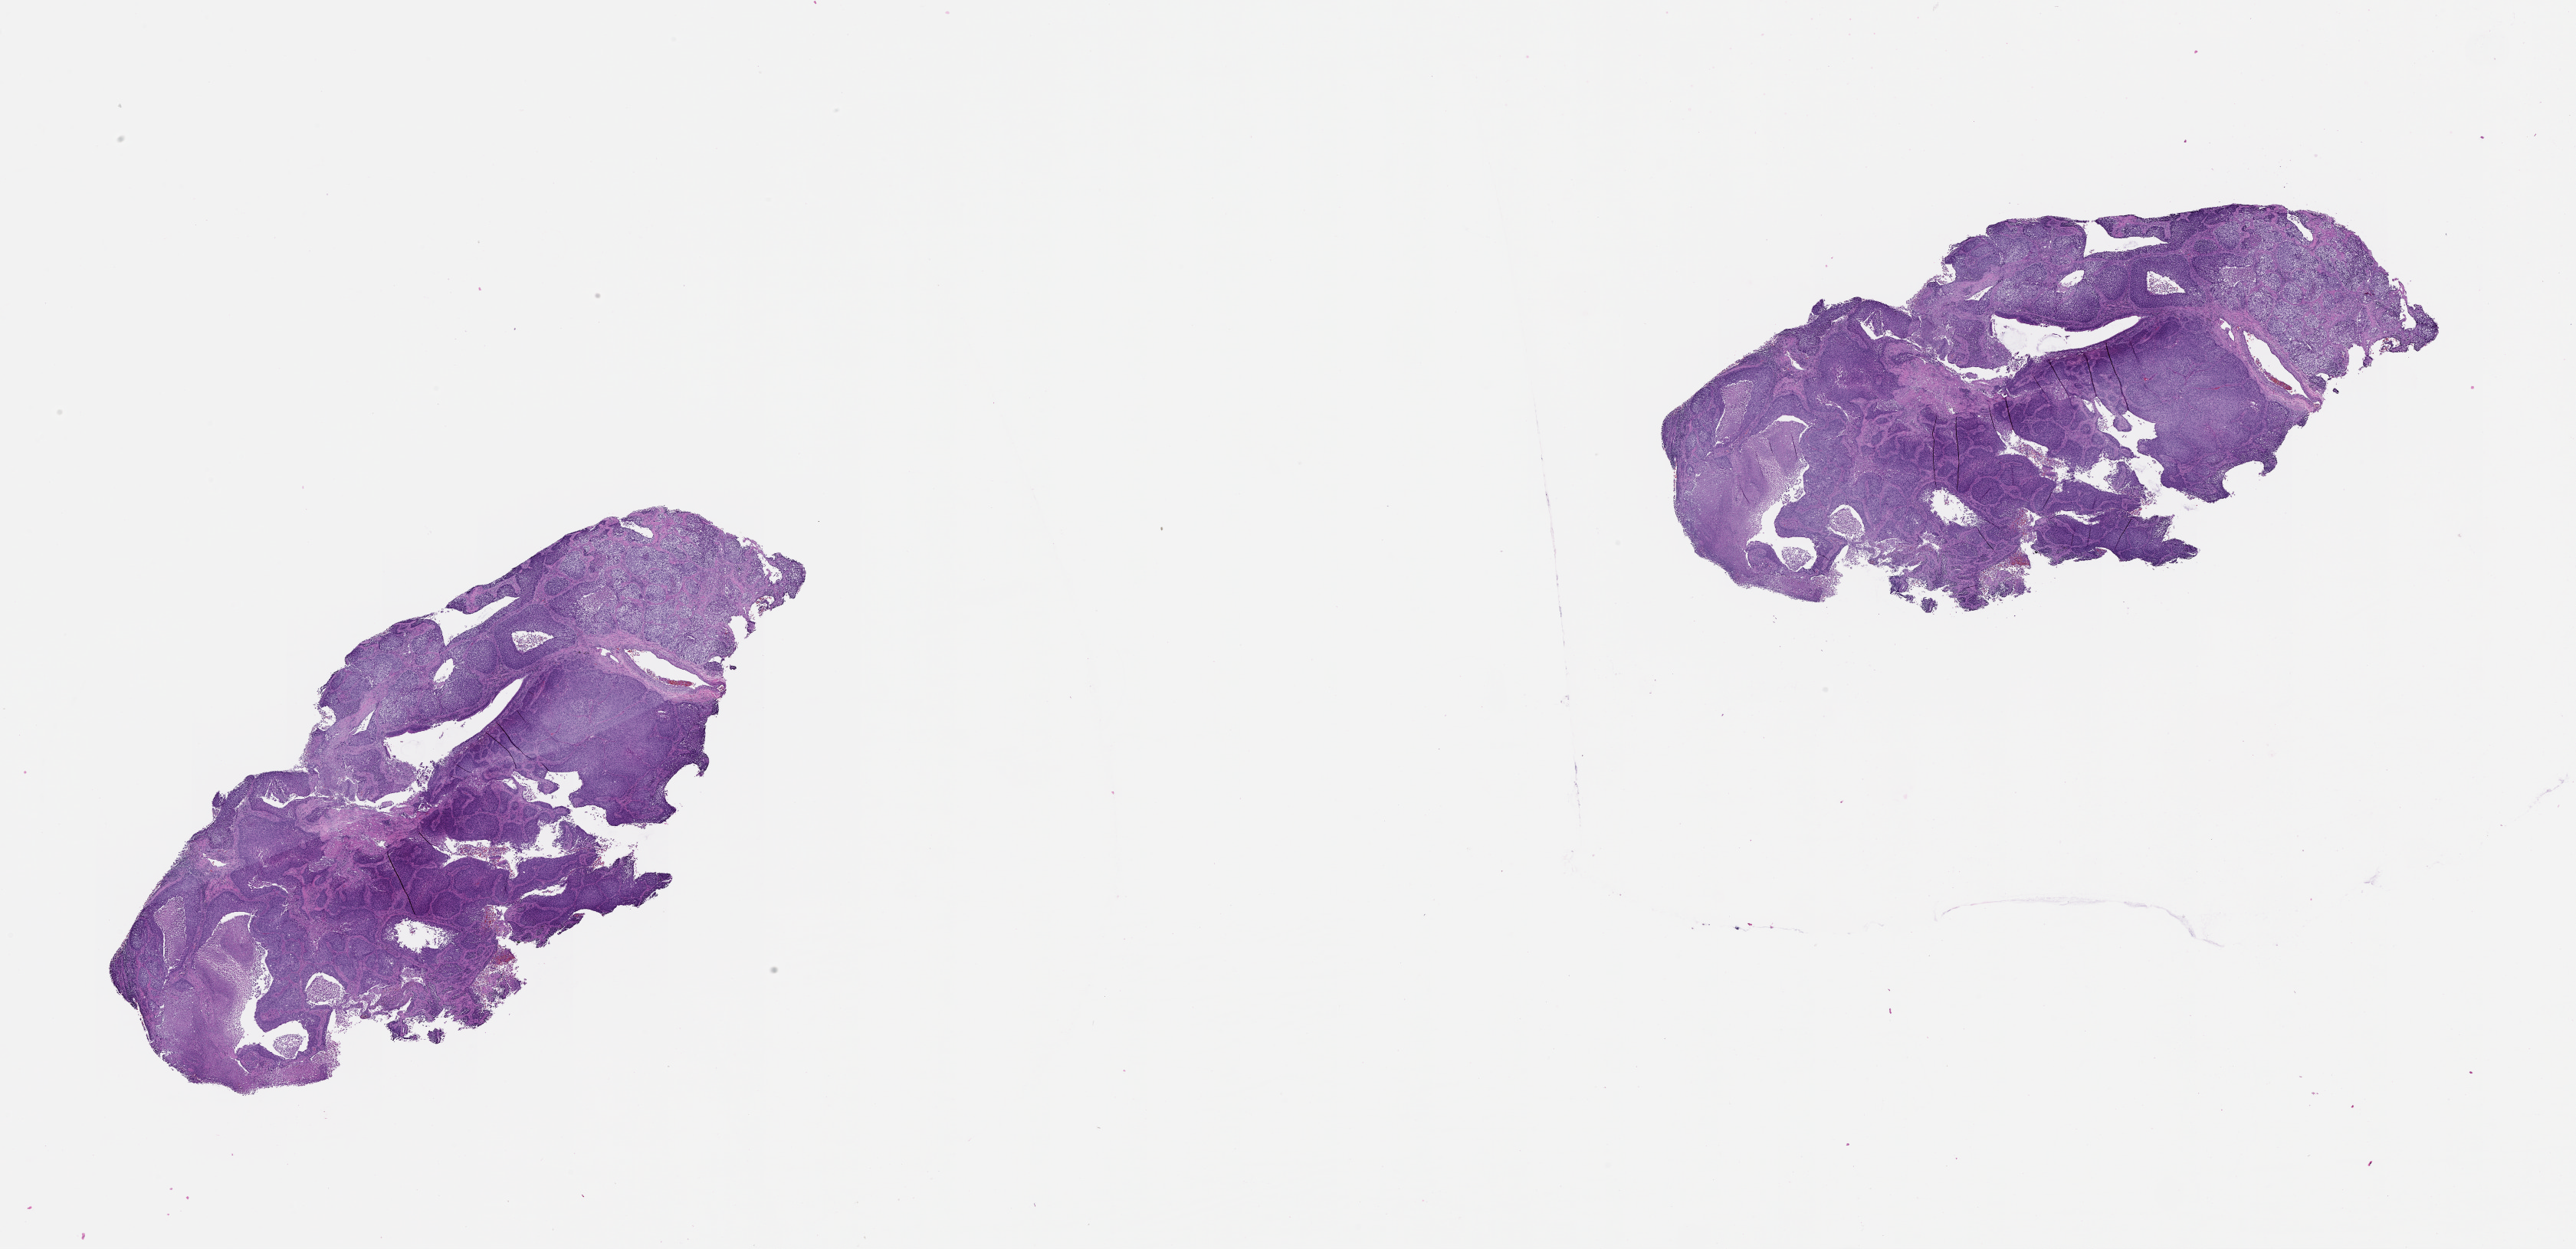
H&E whole-slide image, shown as a low-resolution overview of the whole scanned area (about 27.1 x 13.1 mm), tumour tissue sample, lung. Female, 71 y/o.
Patient diagnosis (cohort enrolment): squamous cell carcinoma (lung).